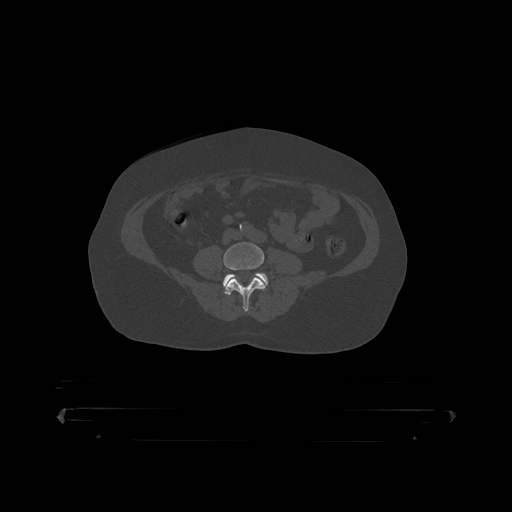
CT including the spine, one axial slice; position 57 of 390 along the scan axis; reconstruction kernel STANDARD; 120 kVp; bone window (W 1800 / L 400 HU); 512 × 512 image matrix, field of view 650 × 650 mm. Patient: male, 60 years. From the clinical record (not read from this slice): primary cancer: prostate.
Annotated regions visible in this slice (semi-automatic segmentation, software-assisted and operator-edited):
- L4 vertebra: box from (x=224, y=242) to (x=265, y=312) px
- L5 vertebra: (x=223, y=273)–(x=269, y=294)